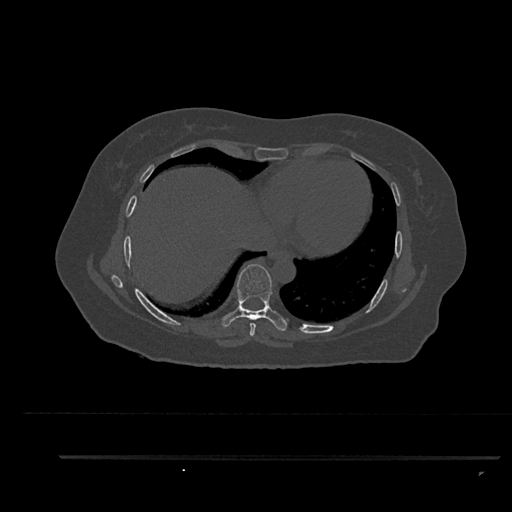
CT including the spine, one axial slice; reconstruction kernel Br40s/3; bone window (W 1800 / L 400 HU); 0.5 mm slice thickness; 512 × 512 image matrix. Female patient, age 44 years. From the clinical record (not read from this slice): primary cancer: renal; vertebrae with lytic lesions (as recorded): L1.
Outlined on this slice (semi-automatic segmentation, software-assisted and operator-edited):
- T7 vertebra: box from (x=249, y=323) to (x=256, y=337) px
- T8 vertebra: (x=221, y=264)–(x=287, y=331)